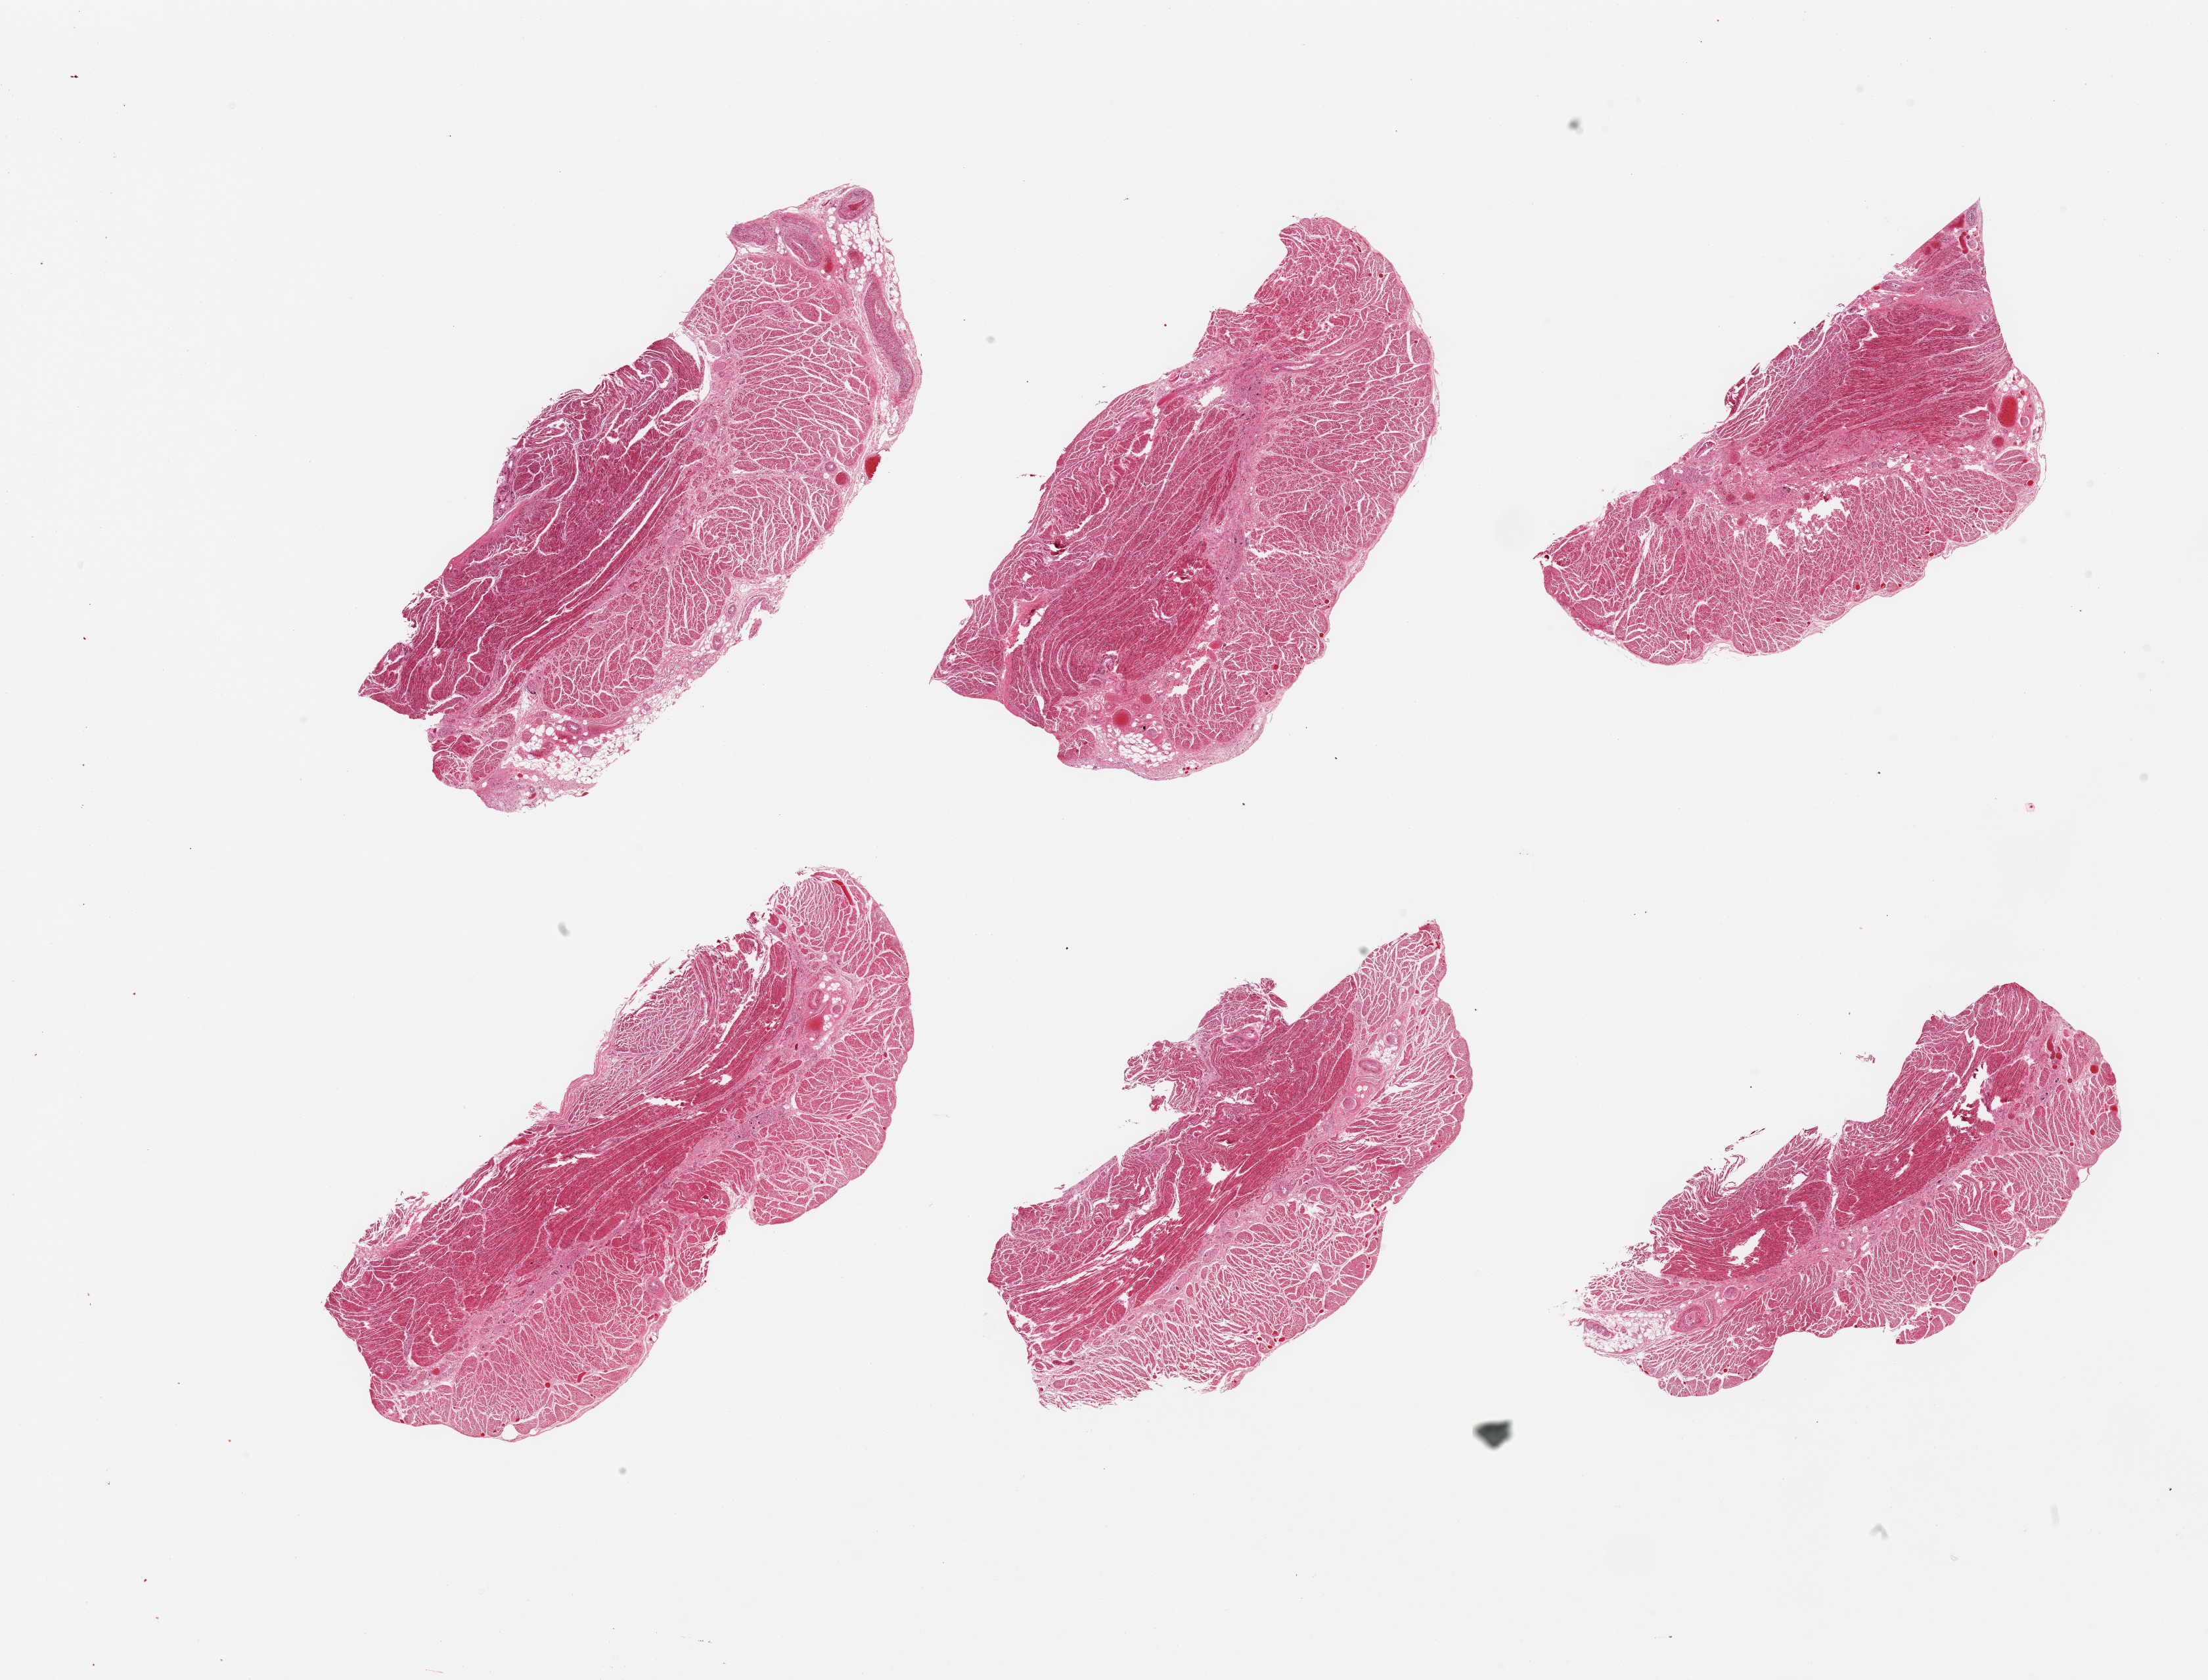
Whole-slide image, H&E stain, brightfield — whole scanned area (about 26.6 x 20.2 mm, slide scanned at 20x) shown as a low-resolution overview. PAXgene-fixed paraffin-embedded (PFPE) section. Section of gastroesophageal junction (target tissue). Donor tissue sample. Donor: male.
* reviewer comment on this tissue sample: 6 pieces, all target muscularis